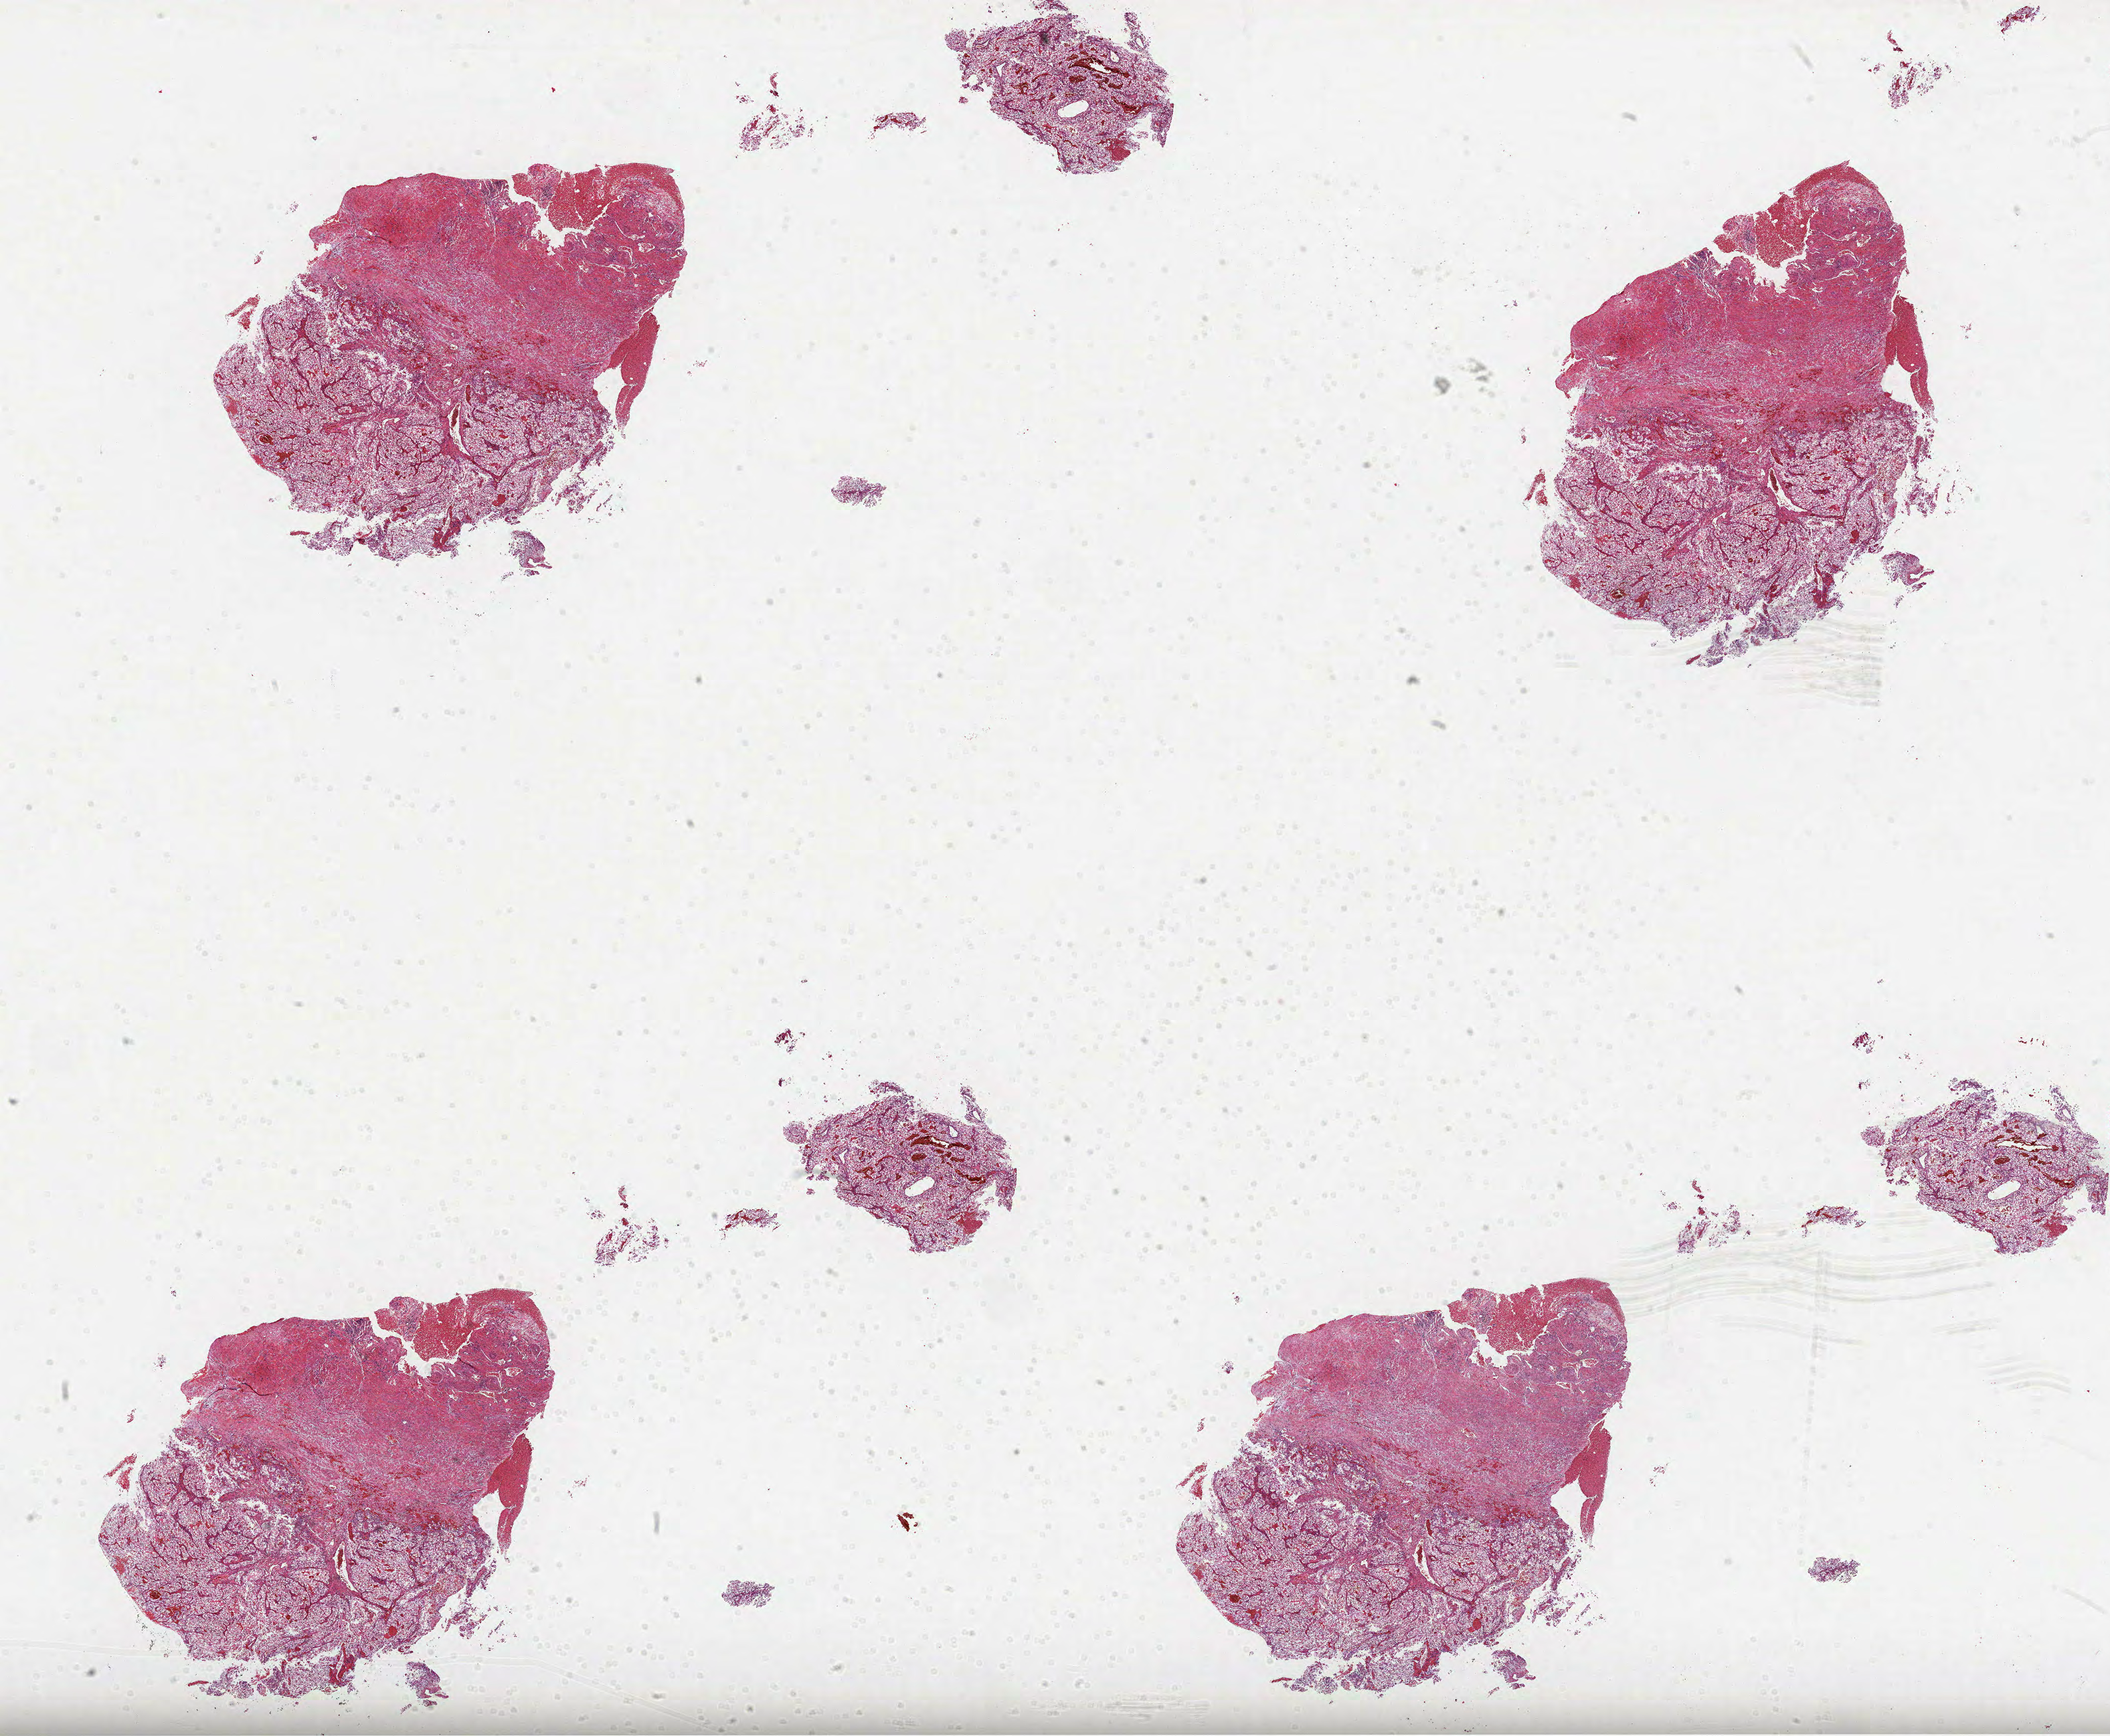
Whole-slide histology image, H&E-stained — low-resolution overview of the scanned area, about 25.6 x 21.1 mm, formalin-fixed paraffin-embedded (FFPE) diagnostic section, sample: primary tumour, kidney. Patient: male, age at initial diagnosis 79 years. Histologic grade: G3 (poorly differentiated).
TNM: T1a N0 M0. Laterality: left. Pathologic diagnosis: Clear cell adenocarcinoma, NOS. AJCC pathologic stage: I.